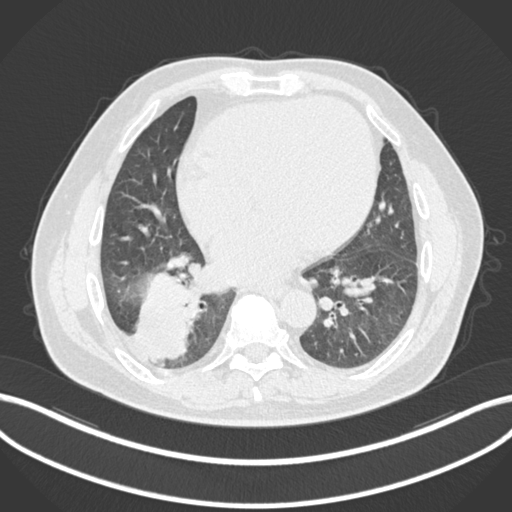
Chest CT, one axial slice; reconstruction kernel B30f; 120 kVp; lung window (W 1500 / L -600 HU); 1 mm slice thickness; 512 × 512 image matrix, field of view 400 × 400 mm. Patient: male, 59 years.
Structures marked on this image (bounding box drawn by a radiologist):
- lung tumour (recorded histology: adenocarcinoma): bounding box (x1, y1, x2, y2) in pixels: (134, 268, 200, 360)